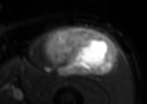
MRI of an extremity soft-tissue mass, one axial slice; position 50 of 85 along the scan axis; T2-weighted fat-saturated; MR volume resampled by the dataset authors to the PET/CT grid (not the native acquisition matrix); 3.27 mm slice thickness; 147 × 104 image matrix, field of view 144 × 102 mm. Male patient. From the clinical record (not read from this slice): histological type: extraskeletal osteosarcoma; grade: high; site of the primary tumour: thigh.
Structures marked on this image (expert contour drawn on MRI and transferred to this co-registered scan by the dataset authors):
- gross tumour volume (mass): box from (x=44, y=26) to (x=116, y=77) px